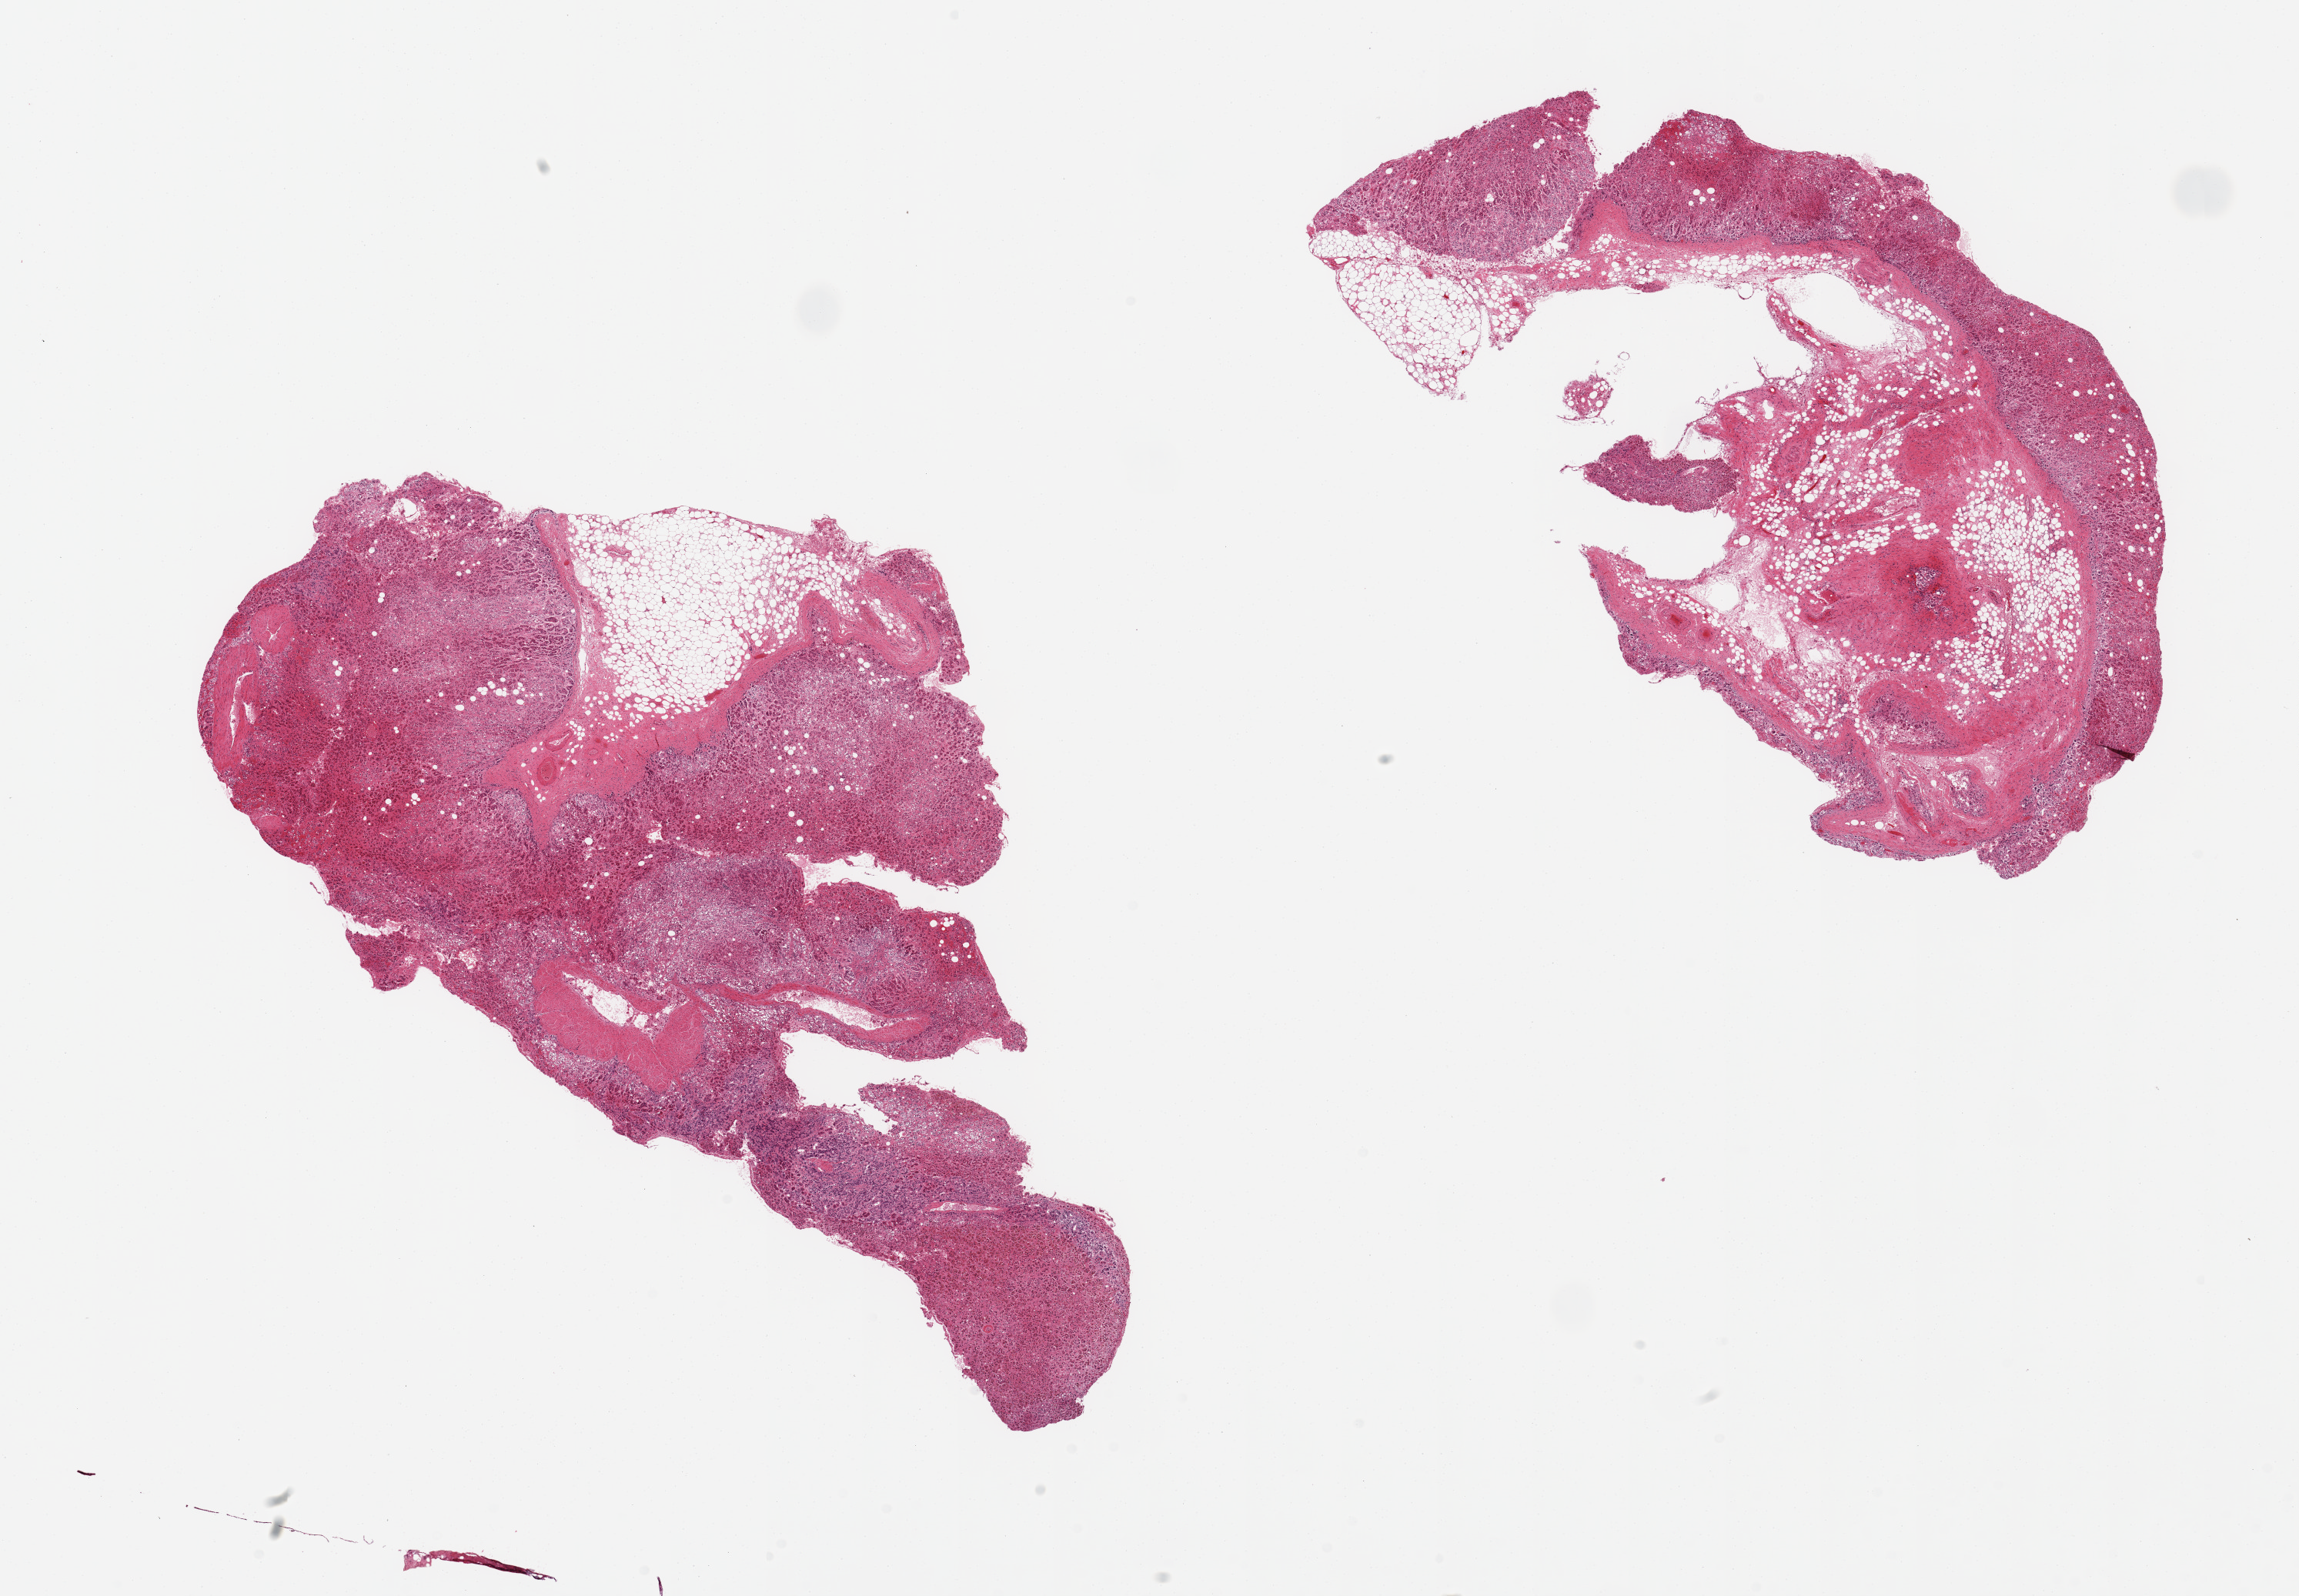
Whole-slide image, hematoxylin and eosin (H&E) stain, brightfield, low-resolution overview of the scanned area, about 23.6 x 16.4 mm. PAXgene-fixed, paraffin-embedded tissue. Section of adrenal gland (target tissue). Donor tissue sample. Donor sex: female.
Reviewer comment on this tissue sample: 2 pieces; 20 & 80% fat content.